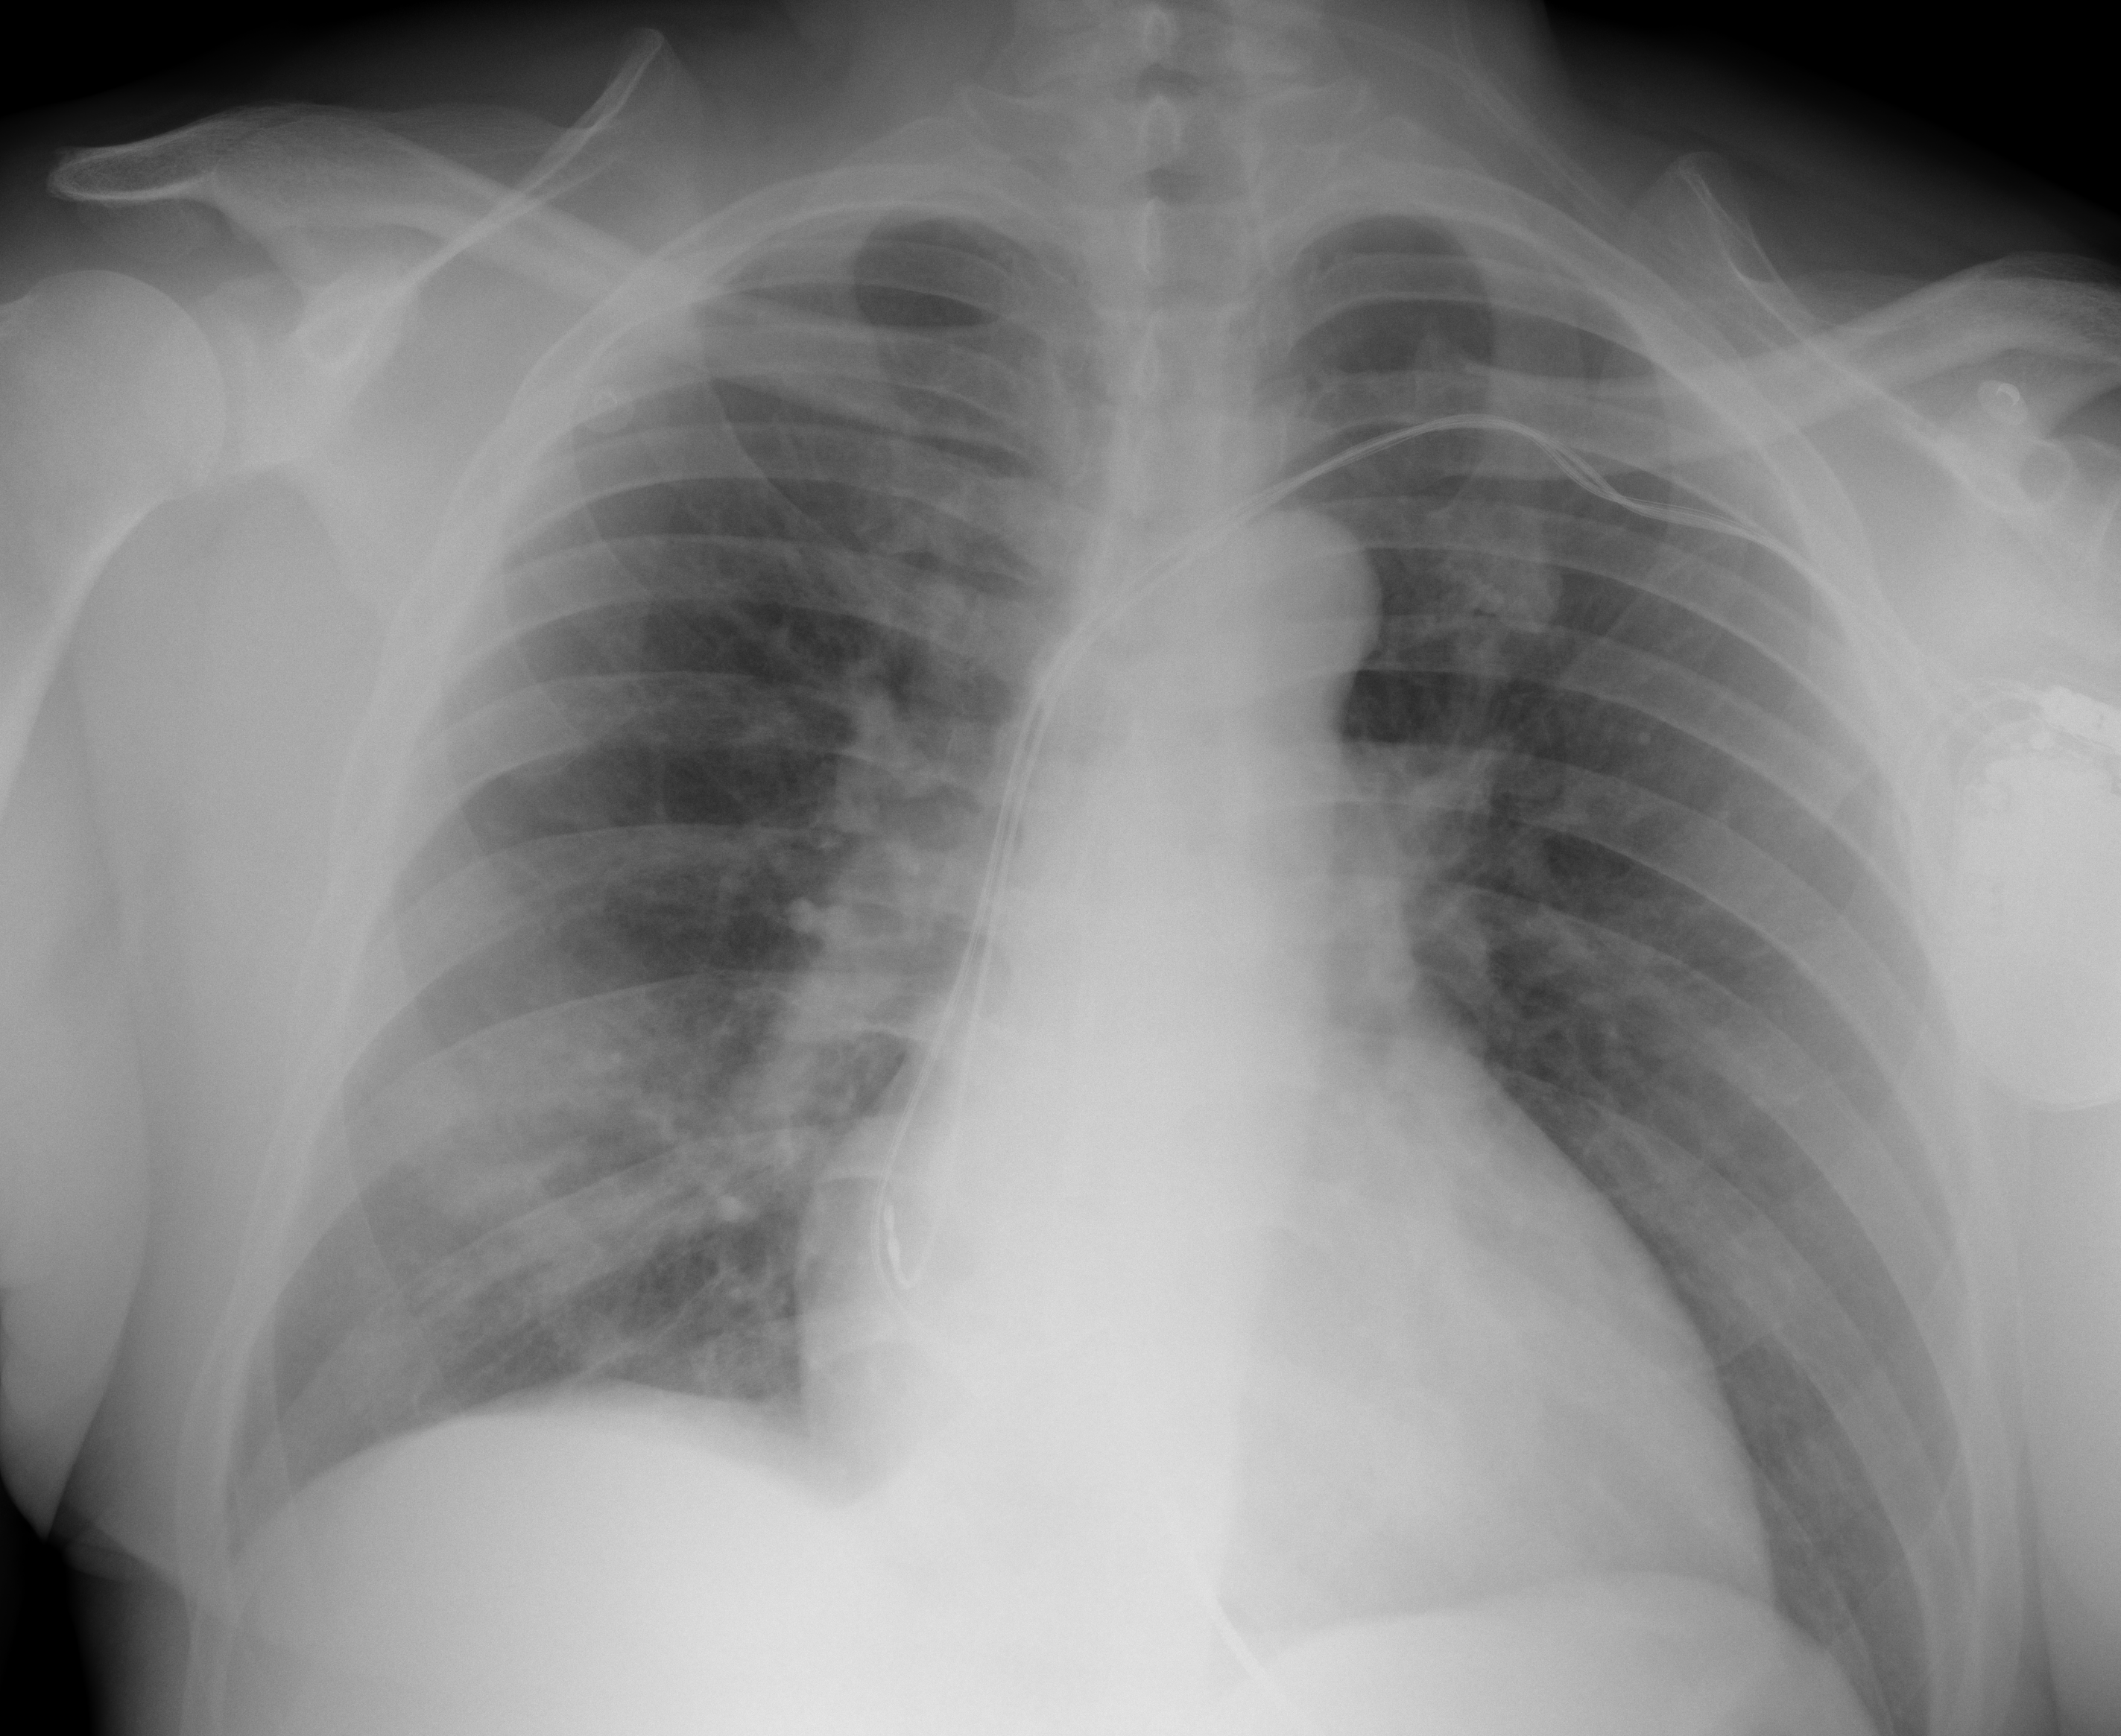
Chest X-ray (portable), AP projection. Male patient, age 60 years; imaged 0 days after the COVID-19 diagnosis.
Radiologist's key findings for this exam: Focal area of consolidation within the right lower lobe.